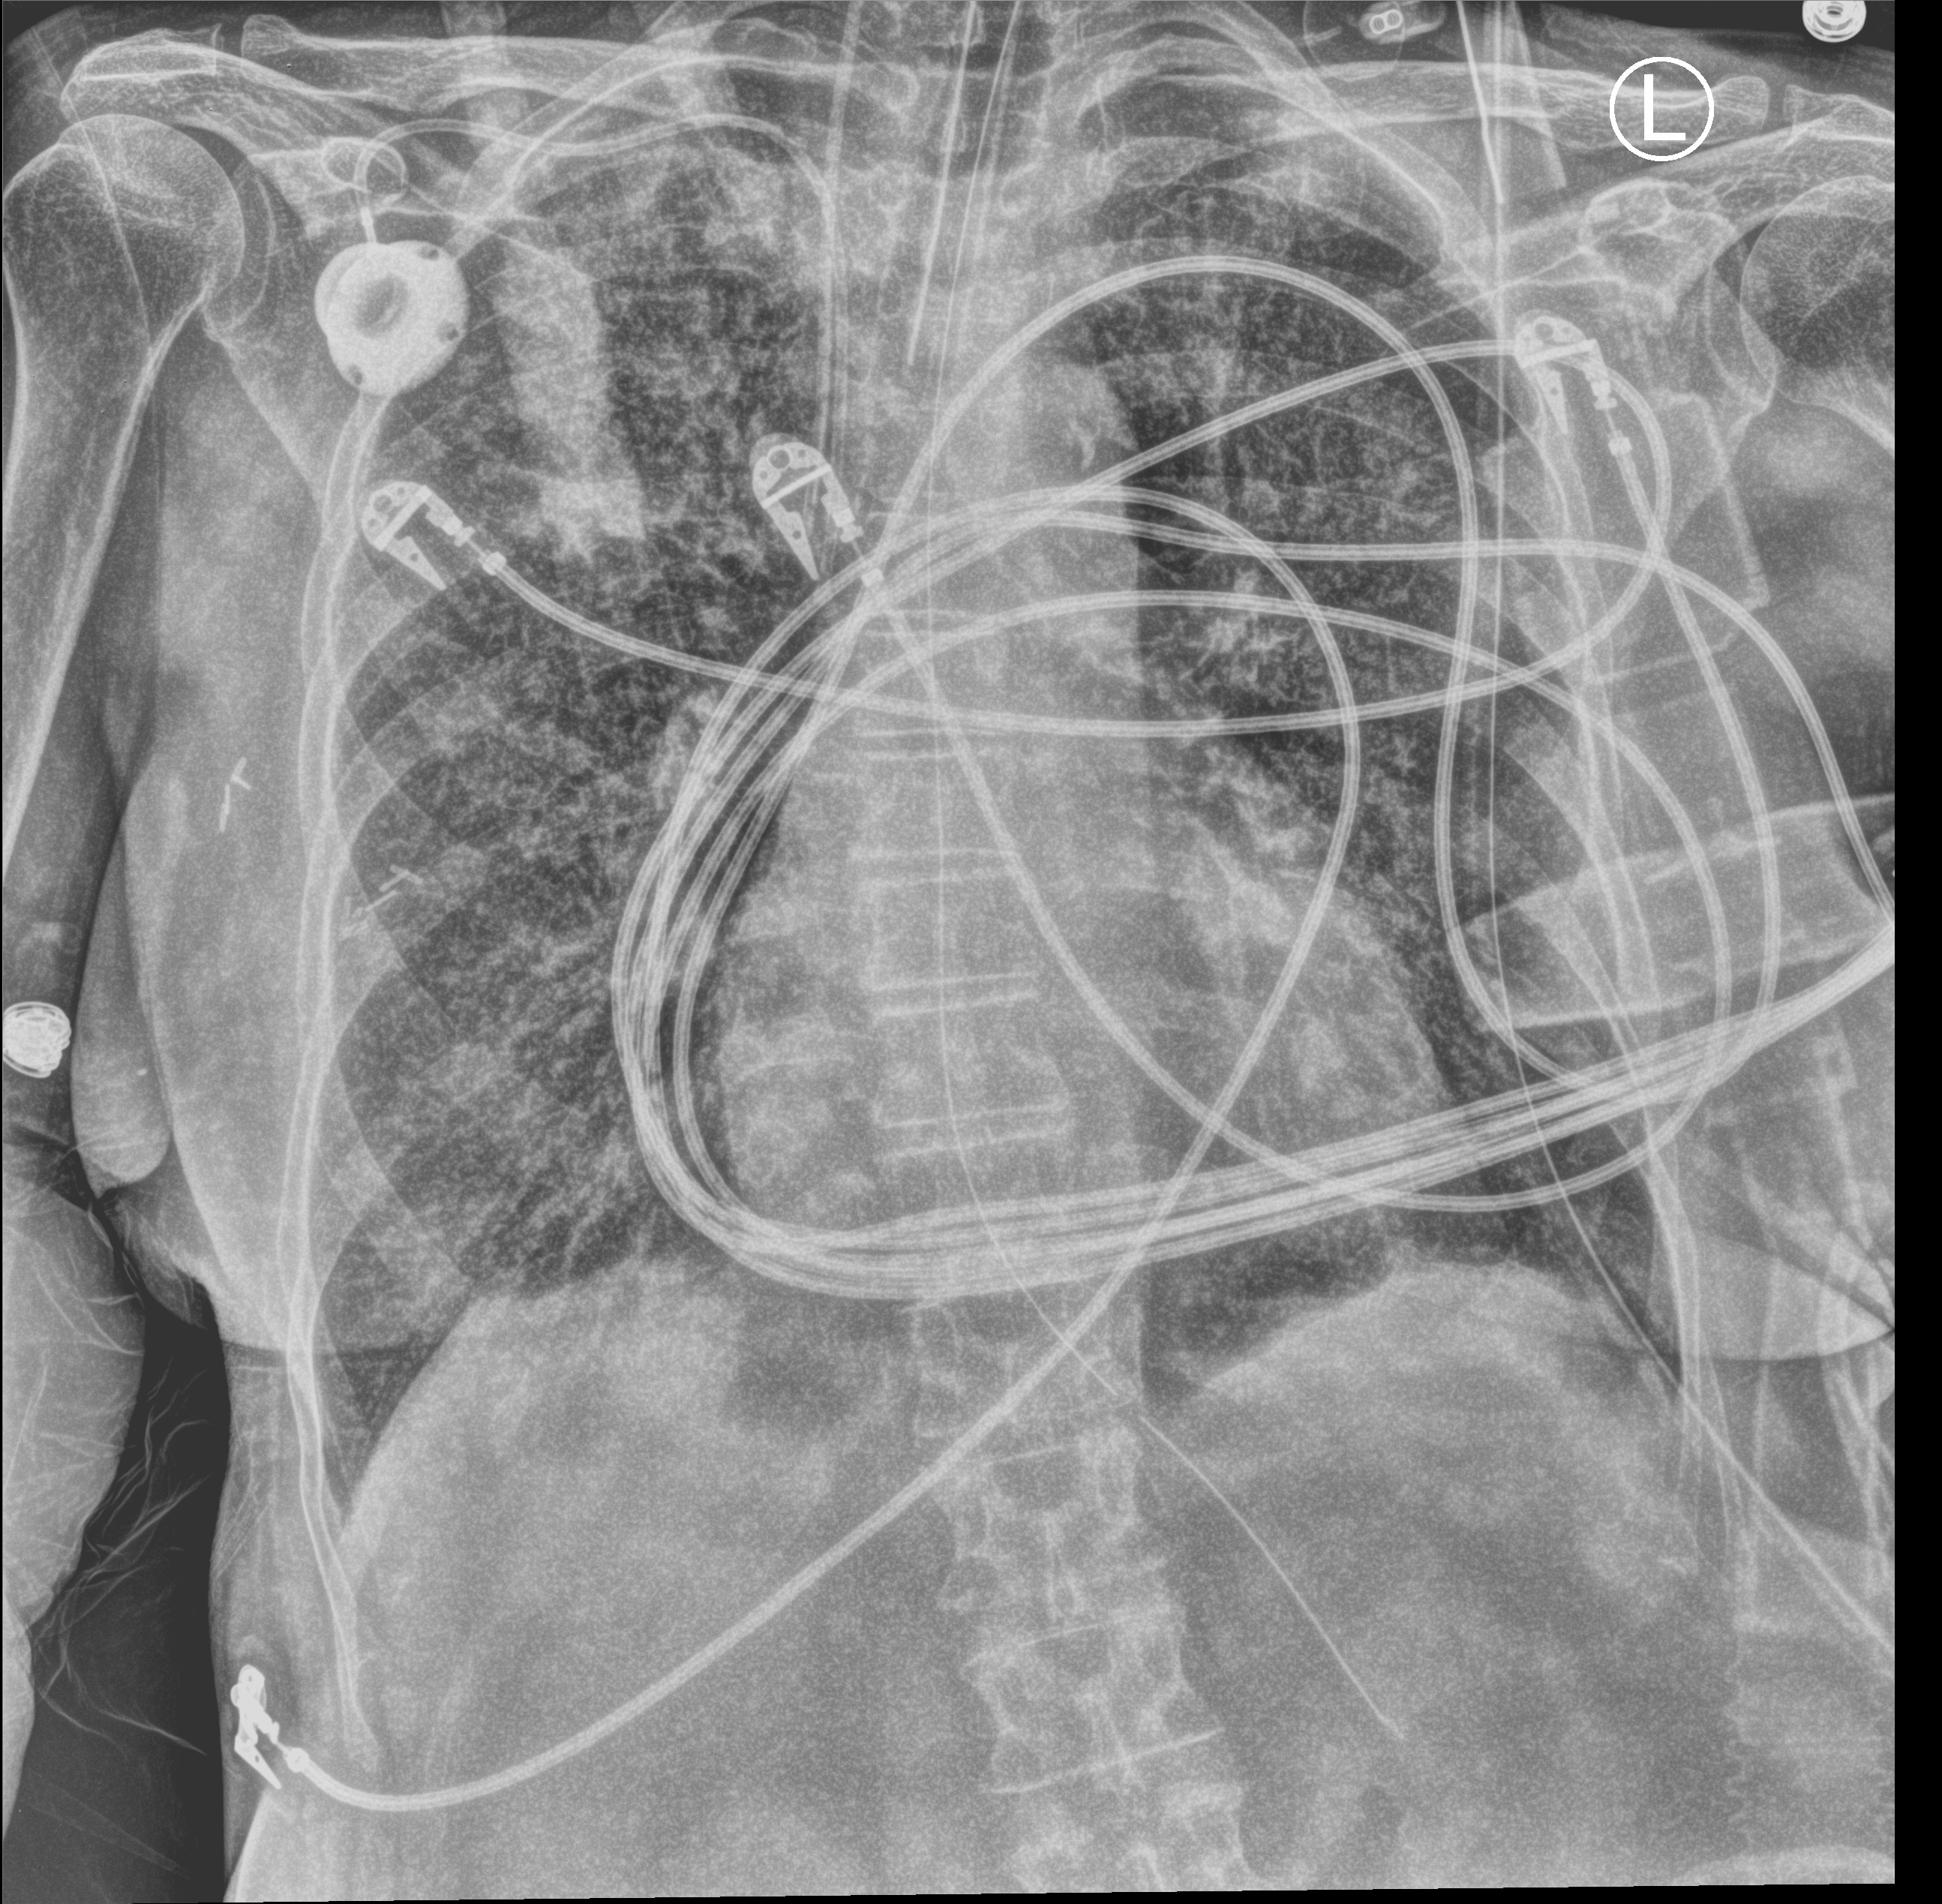
Bedside chest radiograph (computed radiography). Patient hospitalised with COVID-19; female, aged 60–74 years.
Admission-level facts for this patient (not findings on this image; timing relative to this image not recorded): length of hospital stay: 43 days; chronic kidney disease (admission record): no; mechanically ventilated during this hospital stay: yes.